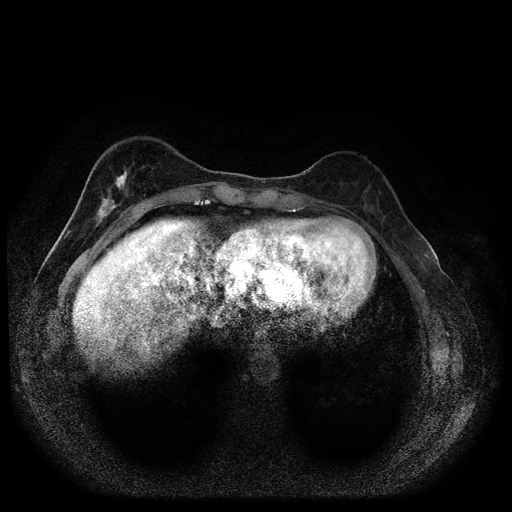
Breast MRI (dynamic contrast-enhanced, multi-phase), one axial slice. Slice 31 of 116 in the series (ordered by position). Dynamic contrast-enhanced series, time point 2 of 5 at this slice position (early post-contrast). 1.5 T. TE 2.7 ms, TR 5.4 ms. 2 mm slice thickness. 512 × 512 image matrix, field of view 330 × 330 mm. Female patient, age 49 years.
Structures marked on this image (semi-automatic segmentation, software-assisted and operator-edited):
- breast lesion (labelled 'tumour' in the annotation; benign lesions carry a separate 'benign' label): bounding box <90,166,130,234> (left, top, right, bottom; pixels)